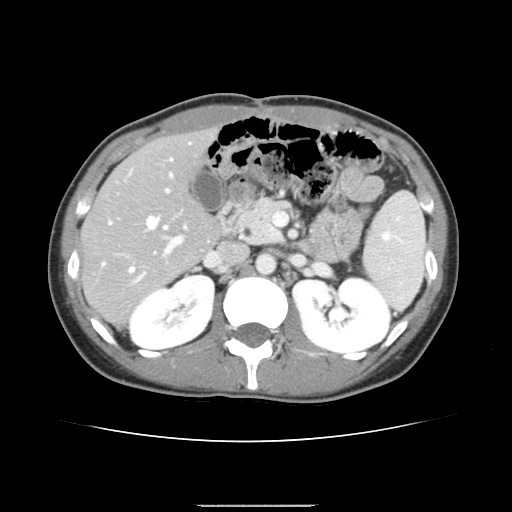
Contrast-enhanced abdominal CT, one axial slice. 120 kVp. Intravenous contrast given. Soft-tissue window (W 400 / L 40 HU). 2.5 mm slice thickness. 512 × 512 image matrix. Female patient, age 32 years. From the clinical record (not read from this slice): diagnosis: colorectal cancer liver metastases, imaged before liver resection; multiple liver metastases: yes; largest metastasis: 0.7 cm; disease in both lobes: no.
Outlined on this slice (expert manual segmentation):
- hepatic veins: bounding box (x1, y1, x2, y2) in pixels: (103, 158, 172, 271)
- liver: (82, 131, 220, 323)
- planned liver remnant (the part of the liver to remain after resection): (82, 131, 220, 277)
- portal vein (with intrahepatic branches): (130, 143, 190, 281)